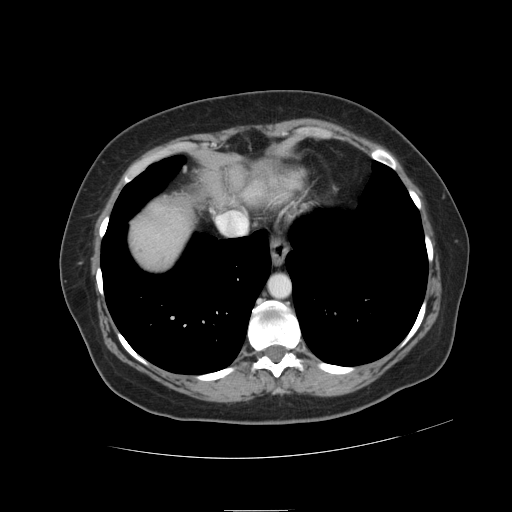
Contrast-enhanced abdominal CT, one axial slice; position 110 of 121 along the scan axis; 120 kVp; intravenous contrast given; soft-tissue window (W 400 / L 40 HU); 512 × 512 image matrix, field of view 400 × 400 mm. Female patient, age 52 years. Case-level facts recorded for this patient, not image findings: diagnosis: colorectal cancer liver metastases, imaged before liver resection; multiple liver metastases: yes; largest metastasis: 6.3 cm; disease in both lobes: no.
Annotated regions visible in this slice (outlined manually by an expert reader):
- liver: bounding box <131,203,191,269> (left, top, right, bottom; pixels)